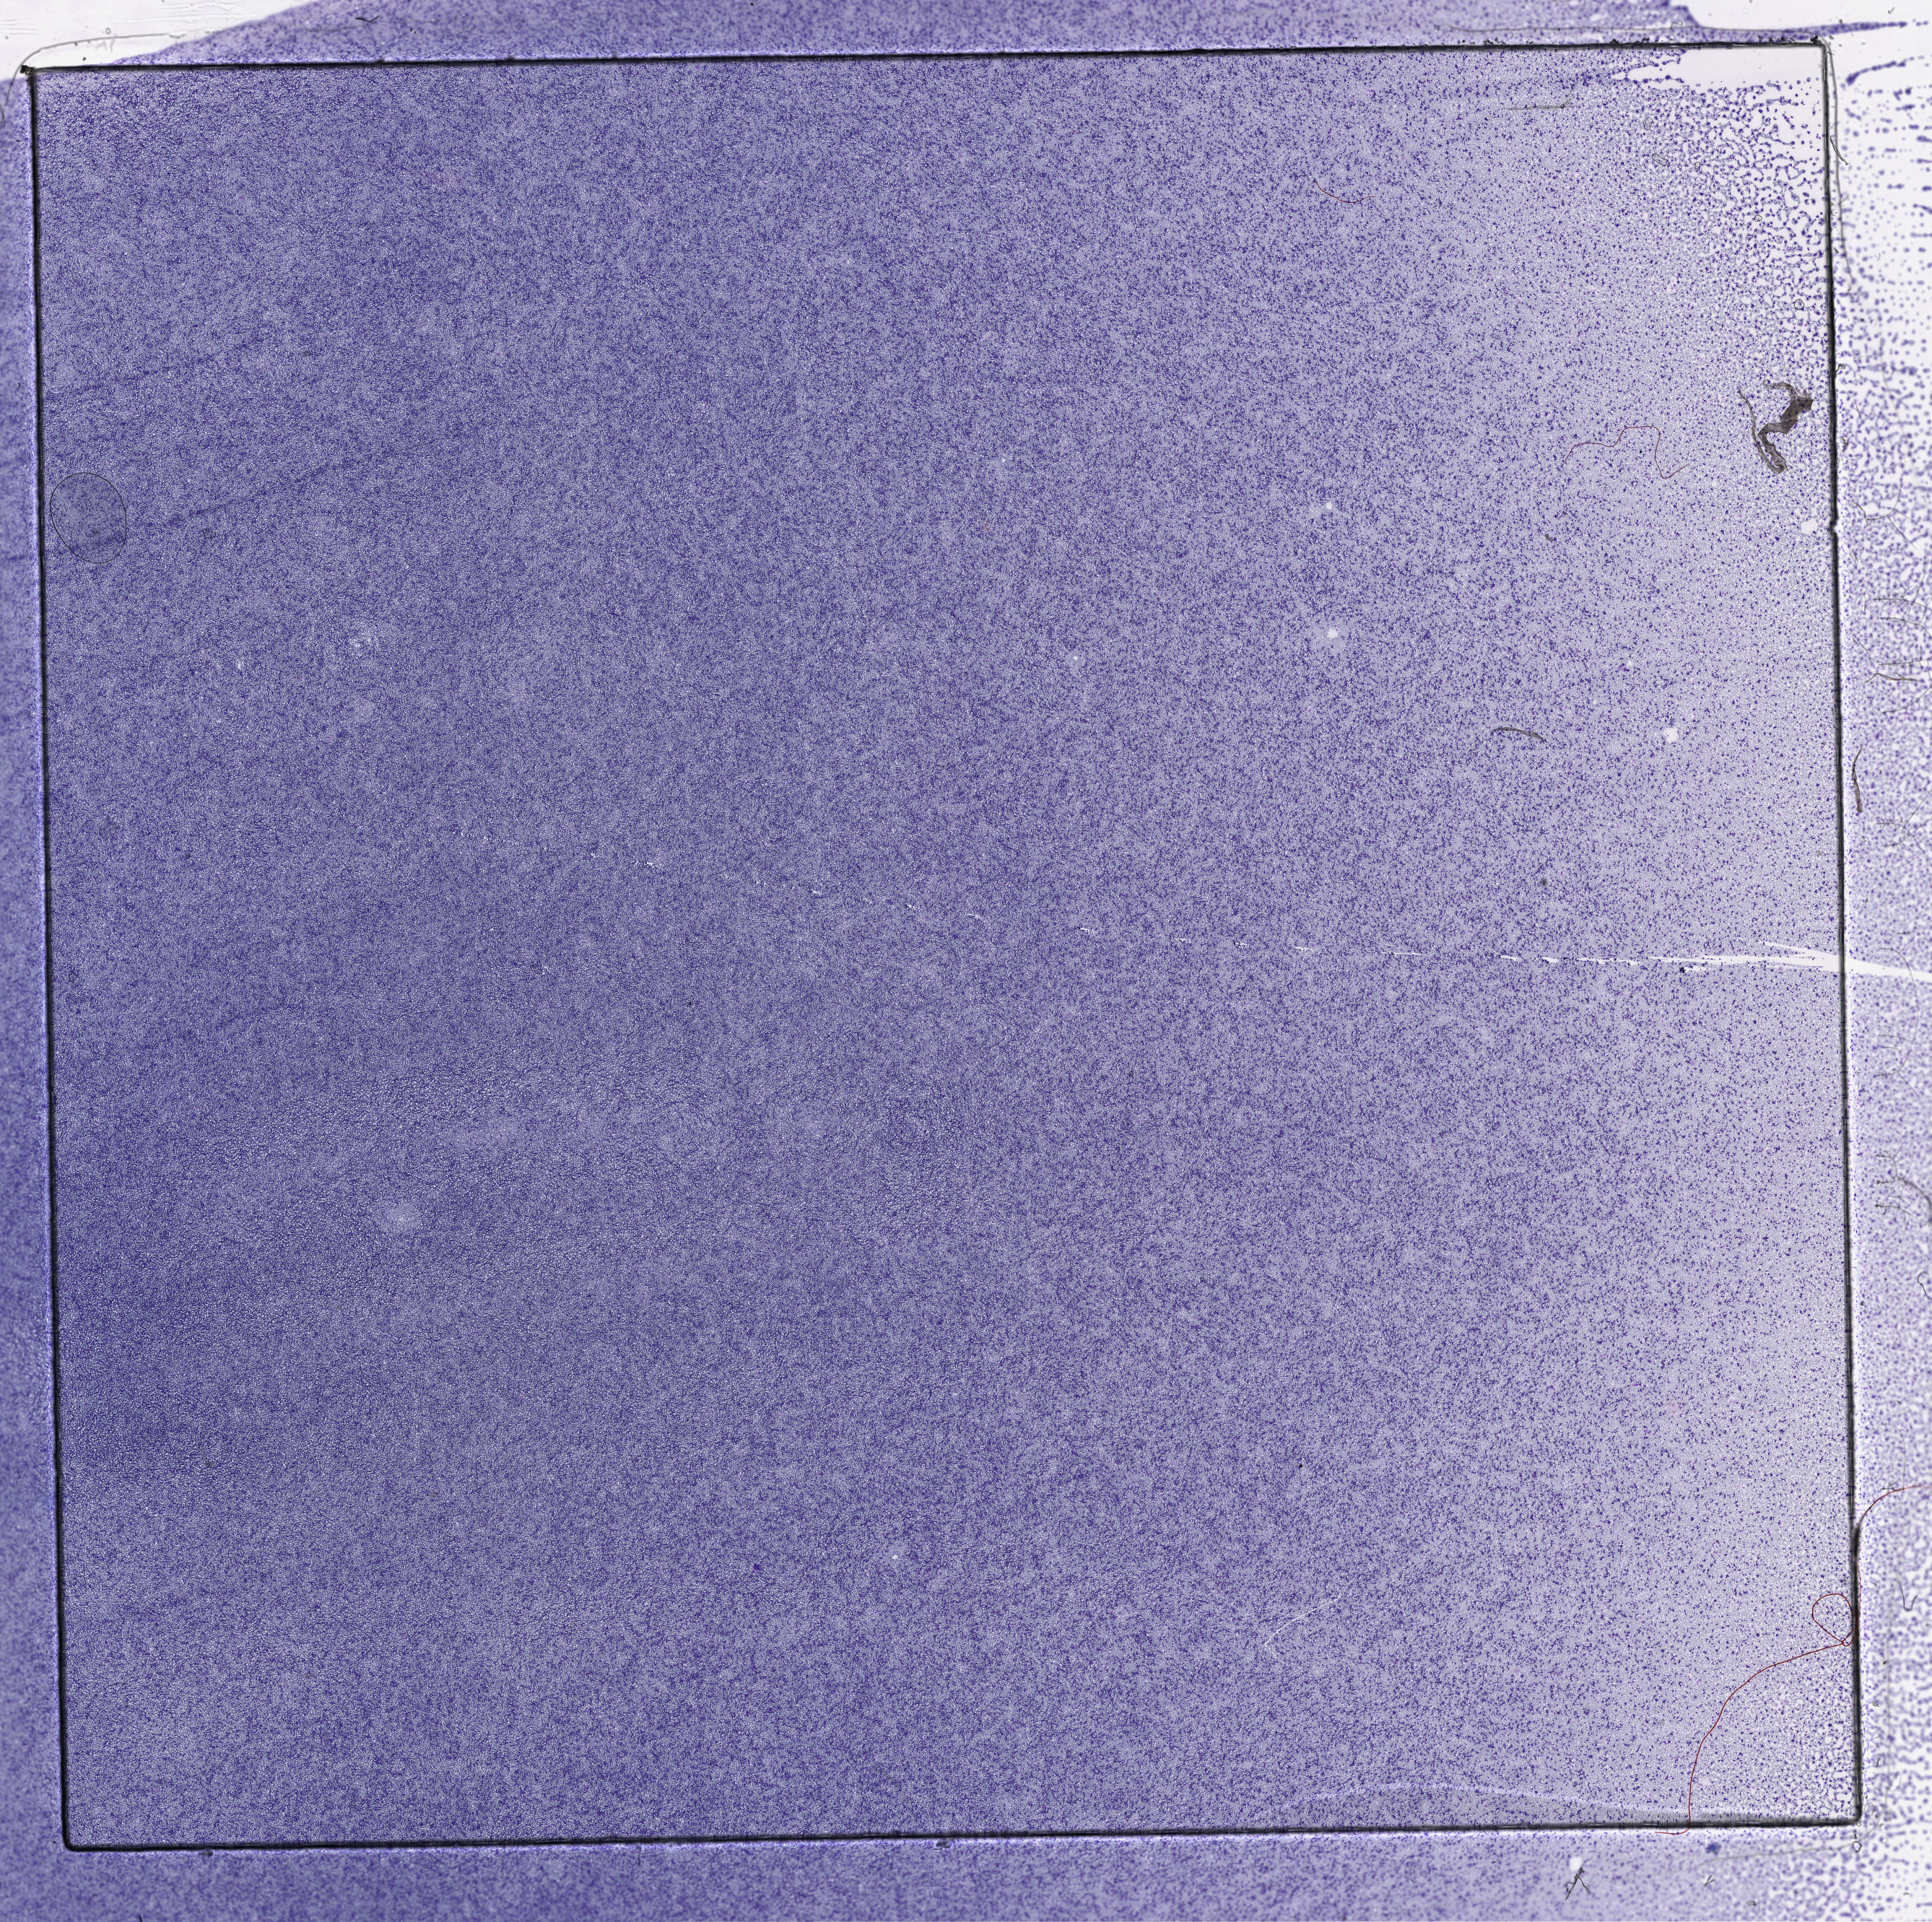
H&E whole-slide image, a low-resolution overview of the entire scanned area, about 21.6 x 21.5 mm. Peripheral blood (leukaemic) sample. 65-year-old female patient.
Diagnosis: Acute Myeloid Leukemia.